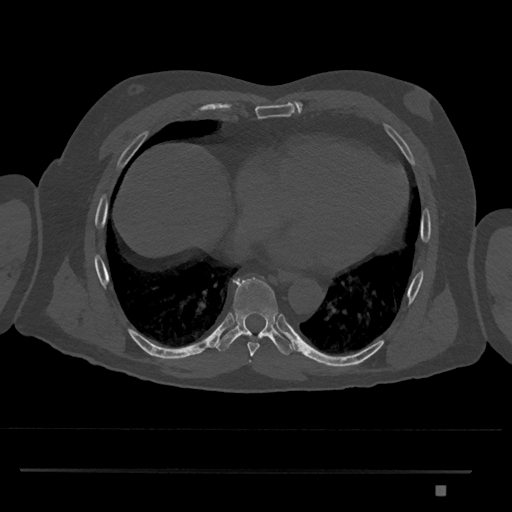
CT including the spine, one axial slice. Slice 1129 of 1134 in the series (ordered by position). Bone window (W 1800 / L 400 HU). 0.5 mm slice thickness. 512 × 512 image matrix, field of view 429 × 429 mm. Male patient, age 65 years. From the clinical record (not read from this slice): primary cancer: prostate.
Annotated regions visible in this slice (semi-automatically segmented with operator editing):
- T8 vertebra: bounding box [x1, y1, x2, y2] px = [215, 277, 295, 356]